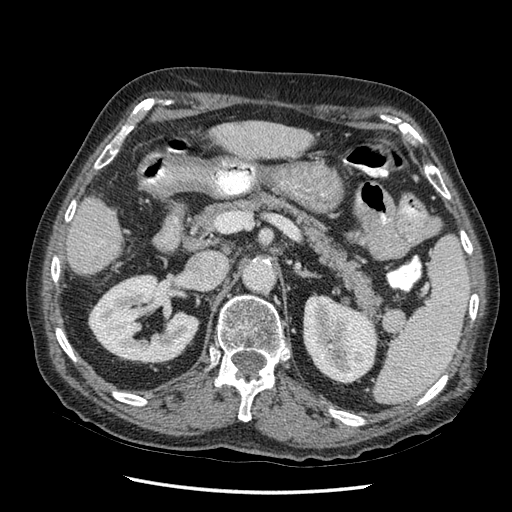
Contrast-enhanced abdominal CT (liver protocol), one axial slice; reconstruction kernel STANDARD; soft-tissue window (W 400 / L 40 HU); 2.5 mm slice thickness; 512 × 512 image matrix, field of view 360 × 360 mm. Case-level facts recorded for this patient, not image findings: diagnosis: hepatocellular carcinoma (patient treated with transarterial chemoembolisation; whether this scan precedes or follows treatment is not stated here); TNM stage (as recorded): Stage-I; Child-Pugh class: A; tumour differentiation: moderately differentiated; tumour nodularity: uninodular.
Annotated regions visible in this slice (semi-automatic segmentation, software-assisted and operator-edited):
- liver parenchyma outside the tumour (the mass and vessels are separate outlines, so this box may not span the whole liver): bounding box <70,120,322,276> (left, top, right, bottom; pixels)
- liver vessels: <251,137,253,140>